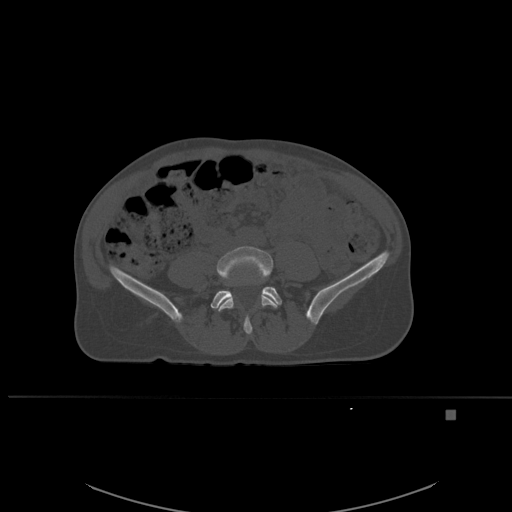
CT including the spine, one axial slice. Slice 182 of 537 in the series (ordered by position). Bone window (W 1800 / L 400 HU). 512 × 512 image matrix. Patient: female, 45 years. From the clinical record (not read from this slice): primary cancer: lung.
Annotated regions visible in this slice (semi-automatic segmentation, software-assisted and operator-edited):
- L4 vertebra: box from (x=214, y=246) to (x=278, y=334) px
- L5 vertebra: (x=210, y=286)–(x=282, y=308)